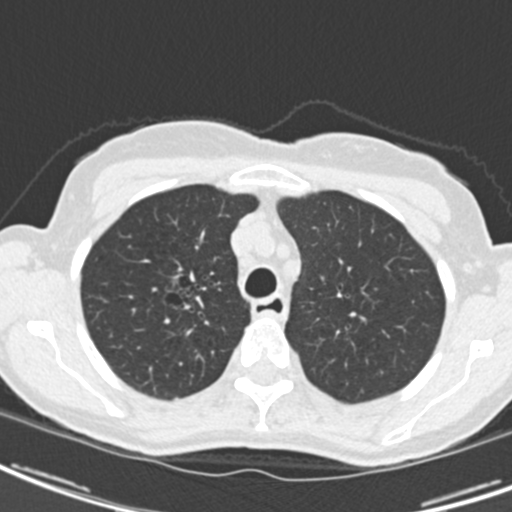
Low-dose screening chest CT, one axial slice. Position 154 of 189 along the scan axis. Reconstruction kernel B30f. Lung window (W 1500 / L -600 HU). 2 mm slice thickness. 512 × 512 image matrix.
Outlined on this slice (expert manual segmentation):
- lesion 1 (tumor, upper lobe of right lung): bounding box [x1, y1, x2, y2] px = [164, 278, 200, 304]